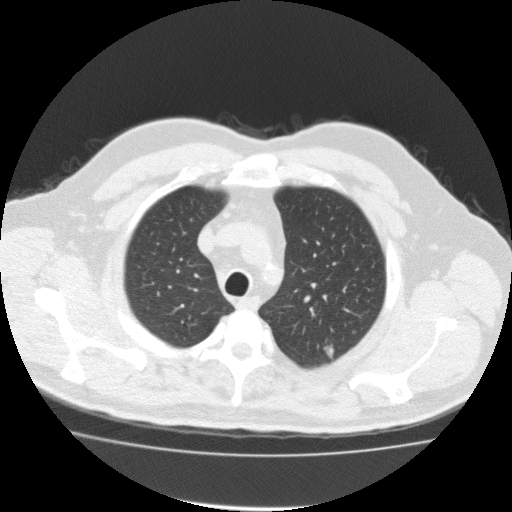
Low-dose screening chest CT, one axial slice. Slice 136 of 161 in the series (ordered by position). Reconstruction kernel FC10. 120 kVp. Lung window (W 1500 / L -600 HU). 2 mm slice thickness. 512 × 512 image matrix.
Outlined on this slice (manually delineated by an expert):
- lesion 1 (tumor, upper lobe of left lung): box from (x=324, y=344) to (x=334, y=359) px